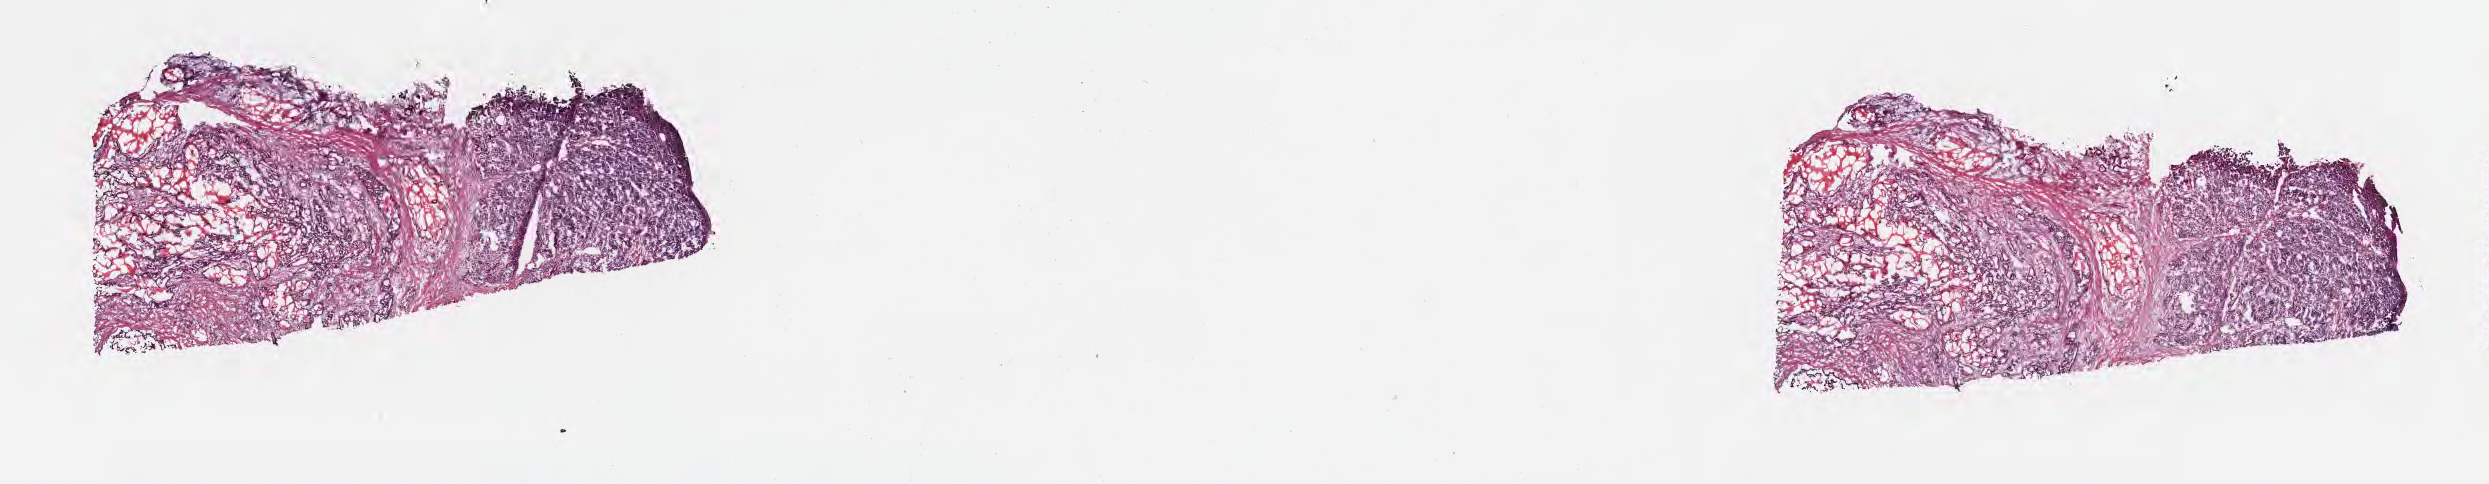
Whole-slide image, haematoxylin and eosin stain, whole scanned area (about 20.1 x 3.9 mm) shown as a low-resolution overview, frozen section, specimen: primary tumor, anatomic site: tail of pancreas. Female, age 63 years at initial diagnosis. Tumor grade: G2 (moderately differentiated). Pathologist review of this section (percent, as recorded): tumor cells 25%, tumor nuclei 25%, stromal cells 25%, necrosis 0%, normal cells 50%. Inflammatory infiltration, as recorded: lymphocyte infiltration 4%, monocyte infiltration 3%, neutrophil infiltration 7%.
Diagnosis: Infiltrating duct carcinoma, NOS. Section: bottom of the tissue portion. AJCC pathologic stage: Stage IIB.